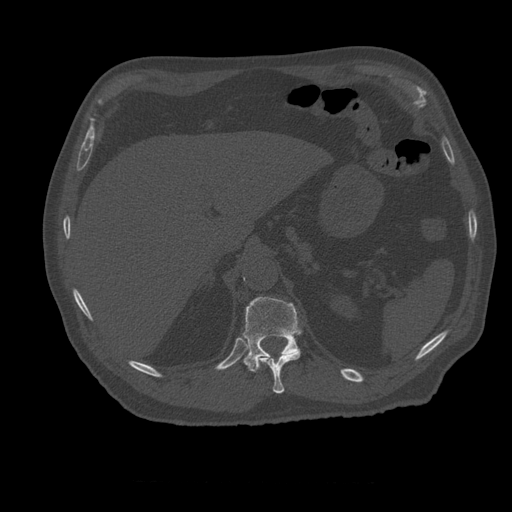
CT including the spine, one axial slice. Position 269 of 399 along the scan axis. Reconstruction kernel STANDARD. 120 kVp. Bone window (W 1800 / L 400 HU). 1.25 mm slice thickness. 512 × 512 image matrix, field of view 407 × 407 mm. Patient age 73 years. Case-level facts recorded for this patient, not image findings: primary cancer: prostate.
Structures marked on this image (semi-automatically segmented with operator editing):
- T11 vertebra: box from (x=259, y=352) to (x=301, y=394) px
- T12 vertebra: (x=243, y=297)–(x=302, y=372)